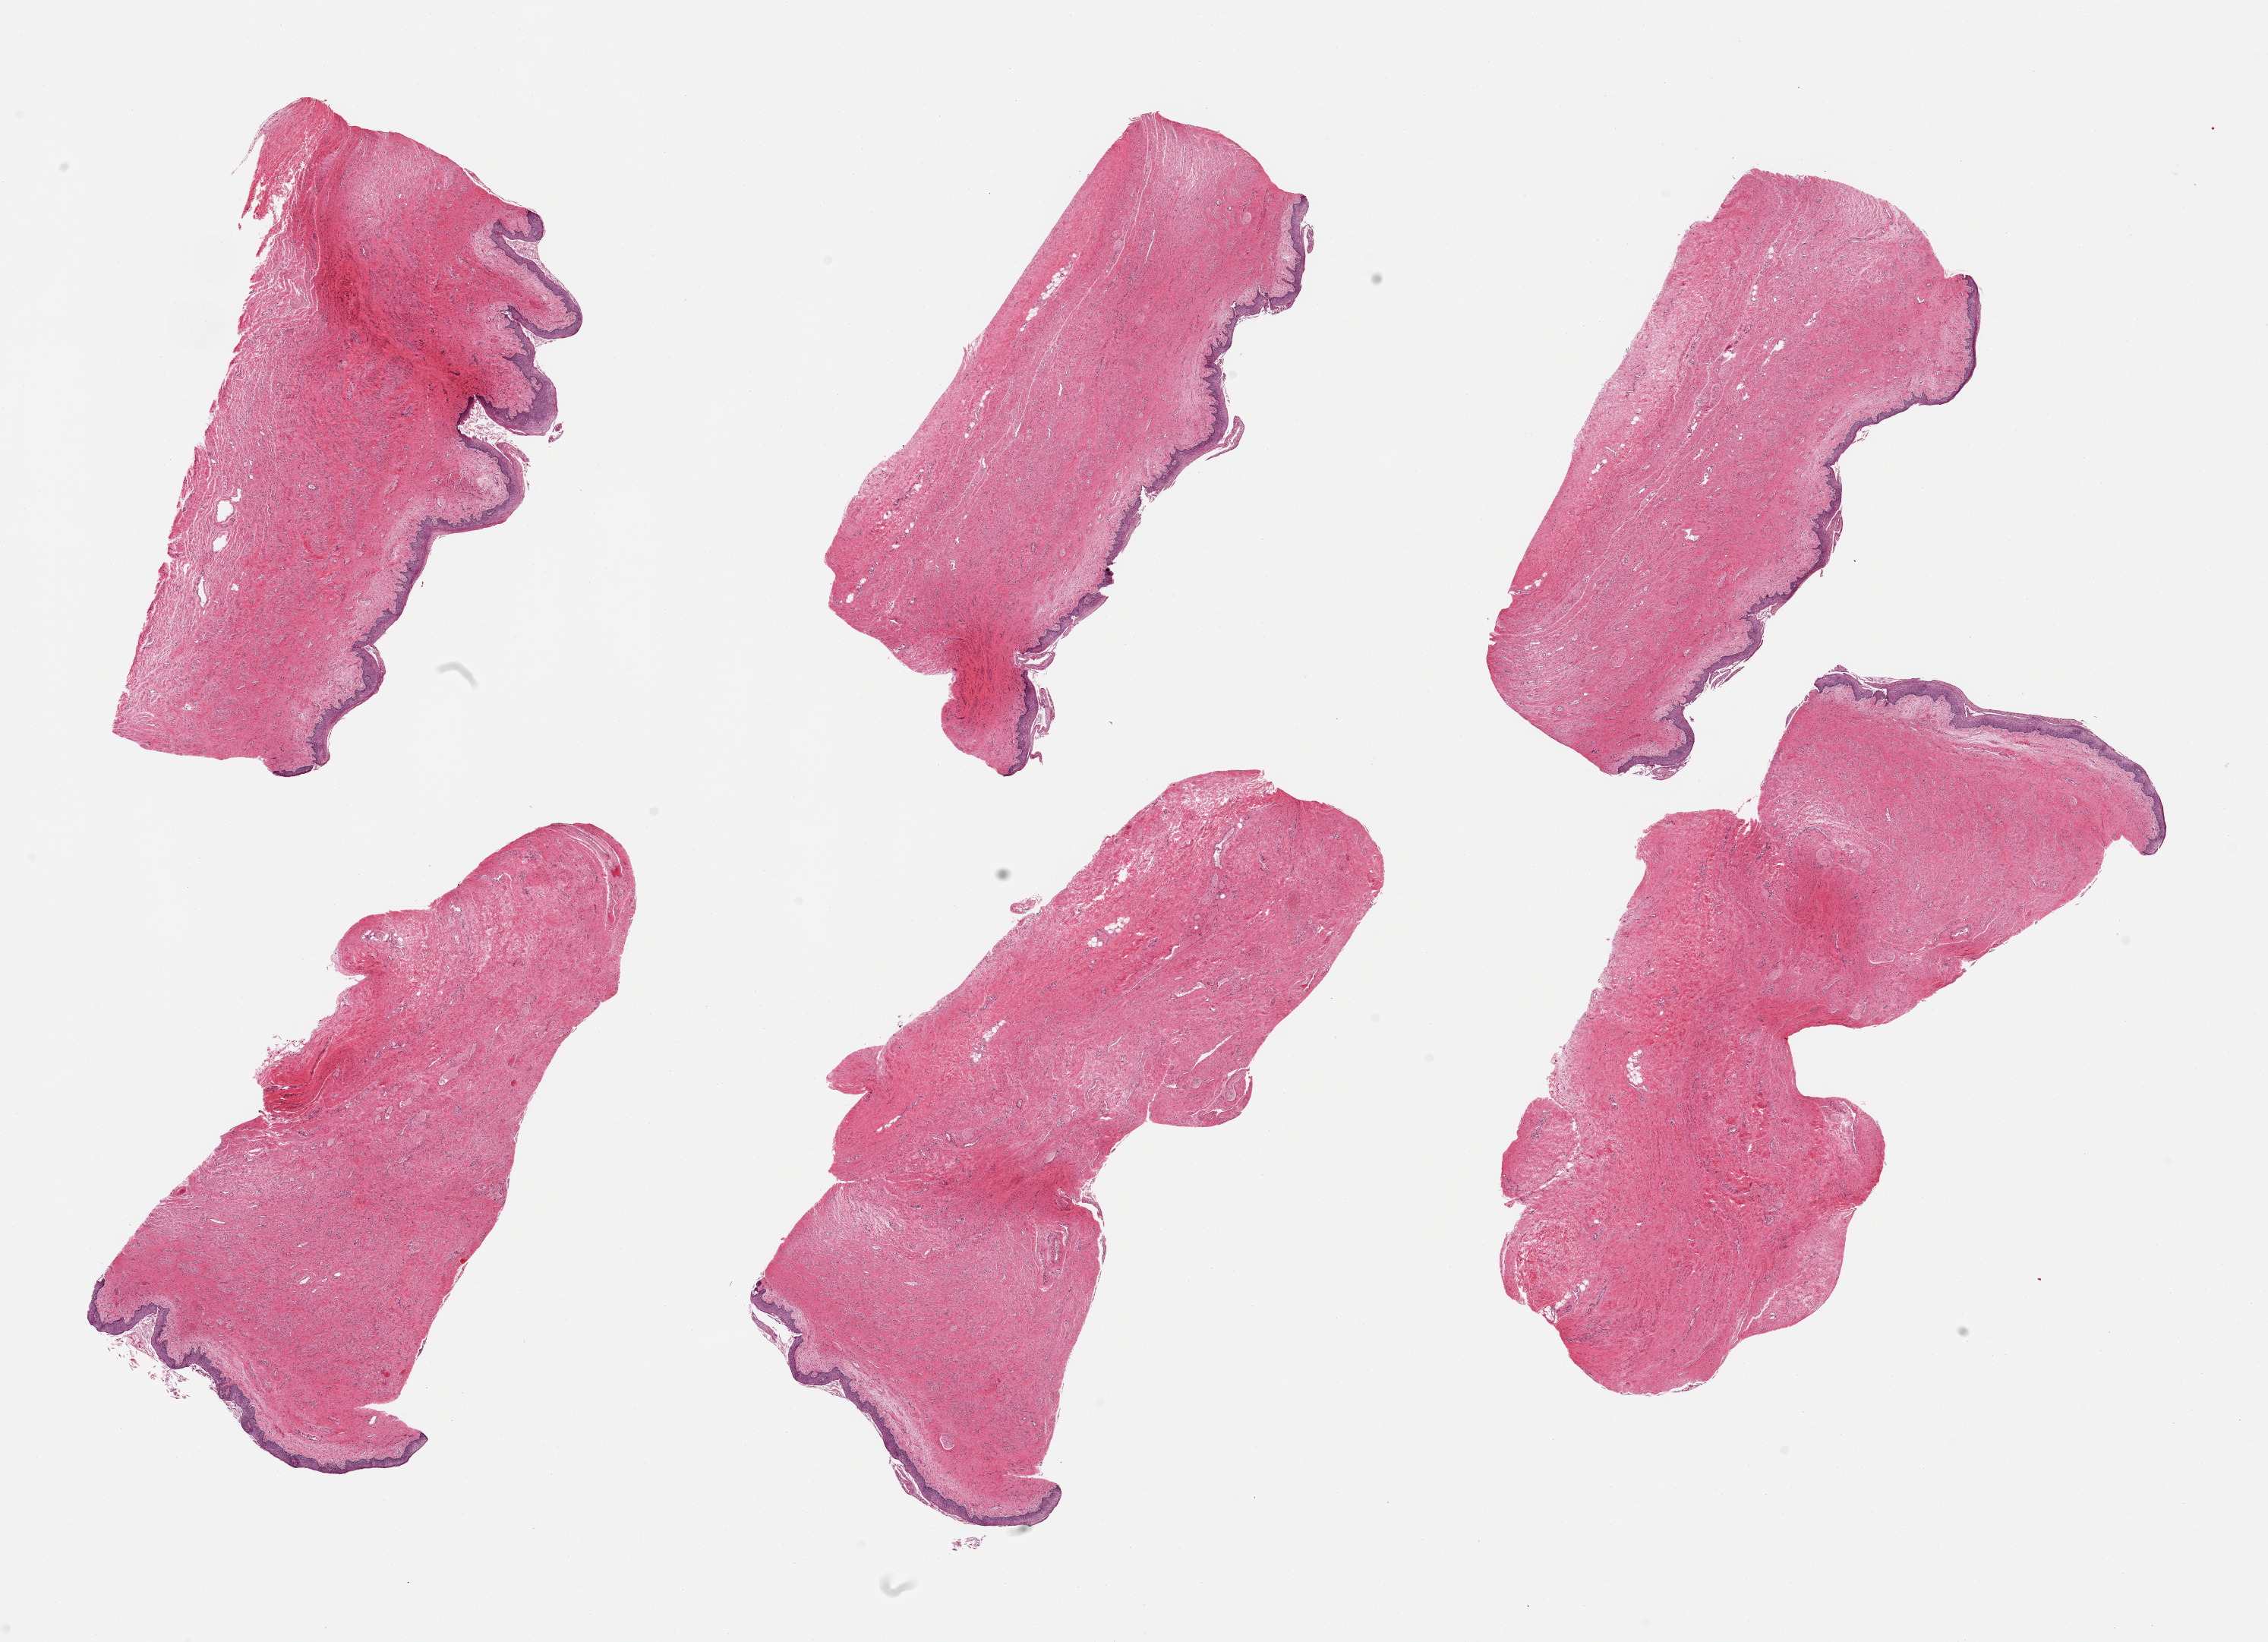
Haematoxylin and eosin whole-slide image — whole scanned area (about 23.6 x 17.1 mm, slide scanned at 20x) shown as a low-resolution overview, PAXgene-fixed paraffin-embedded (PFPE) section, sampled site (target tissue): vagina, tissue donor sample.
Review note (as recorded): 6 pieces, squamous epithelium is ~0.1mm, early sloughing.